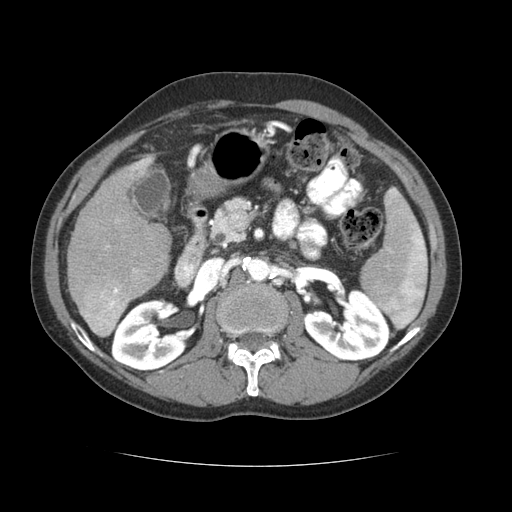
Contrast-enhanced abdominal CT (liver protocol), one axial slice. Position 30 of 69 along the scan axis. Reconstruction kernel STANDARD. Soft-tissue window (W 400 / L 40 HU). 2.5 mm slice thickness. 512 × 512 image matrix, field of view 360 × 360 mm. From the clinical record (not read from this slice): diagnosis: hepatocellular carcinoma (patient treated with transarterial chemoembolisation; whether this scan precedes or follows treatment is not stated here); TNM stage (as recorded): Stage-II; Child-Pugh class: B; tumour differentiation: poorly differentiated; tumour nodularity: multinodular.
Outlined on this slice (semi-automatically segmented with operator editing):
- liver parenchyma outside the tumour (the mass and vessels are separate outlines, so this box may not span the whole liver): bounding box [x1, y1, x2, y2] px = [66, 154, 170, 336]
- mass: [80, 273, 129, 335]
- liver vessels: [117, 159, 151, 273]